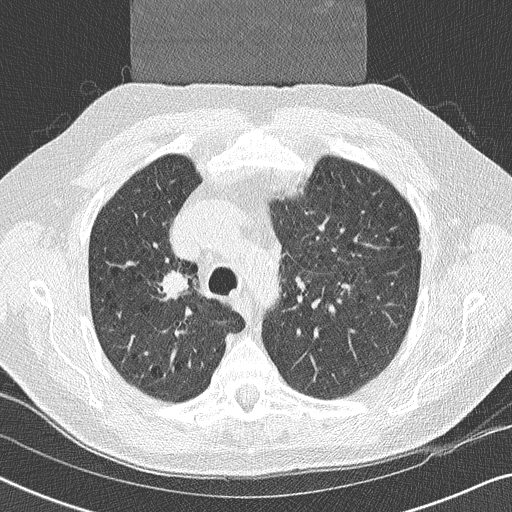
Low-dose screening chest CT, one axial slice; slice 176 of 252 in the series (ordered by position); reconstruction kernel B50f; lung window (W 1500 / L -600 HU); 2 mm slice thickness; 512 × 512 image matrix, field of view 330 × 330 mm.
Annotated regions visible in this slice (outlined manually by an expert reader):
- lesion 1 (tumor, upper lobe of right lung): bounding box (x1, y1, x2, y2) in pixels: (162, 272, 189, 297)